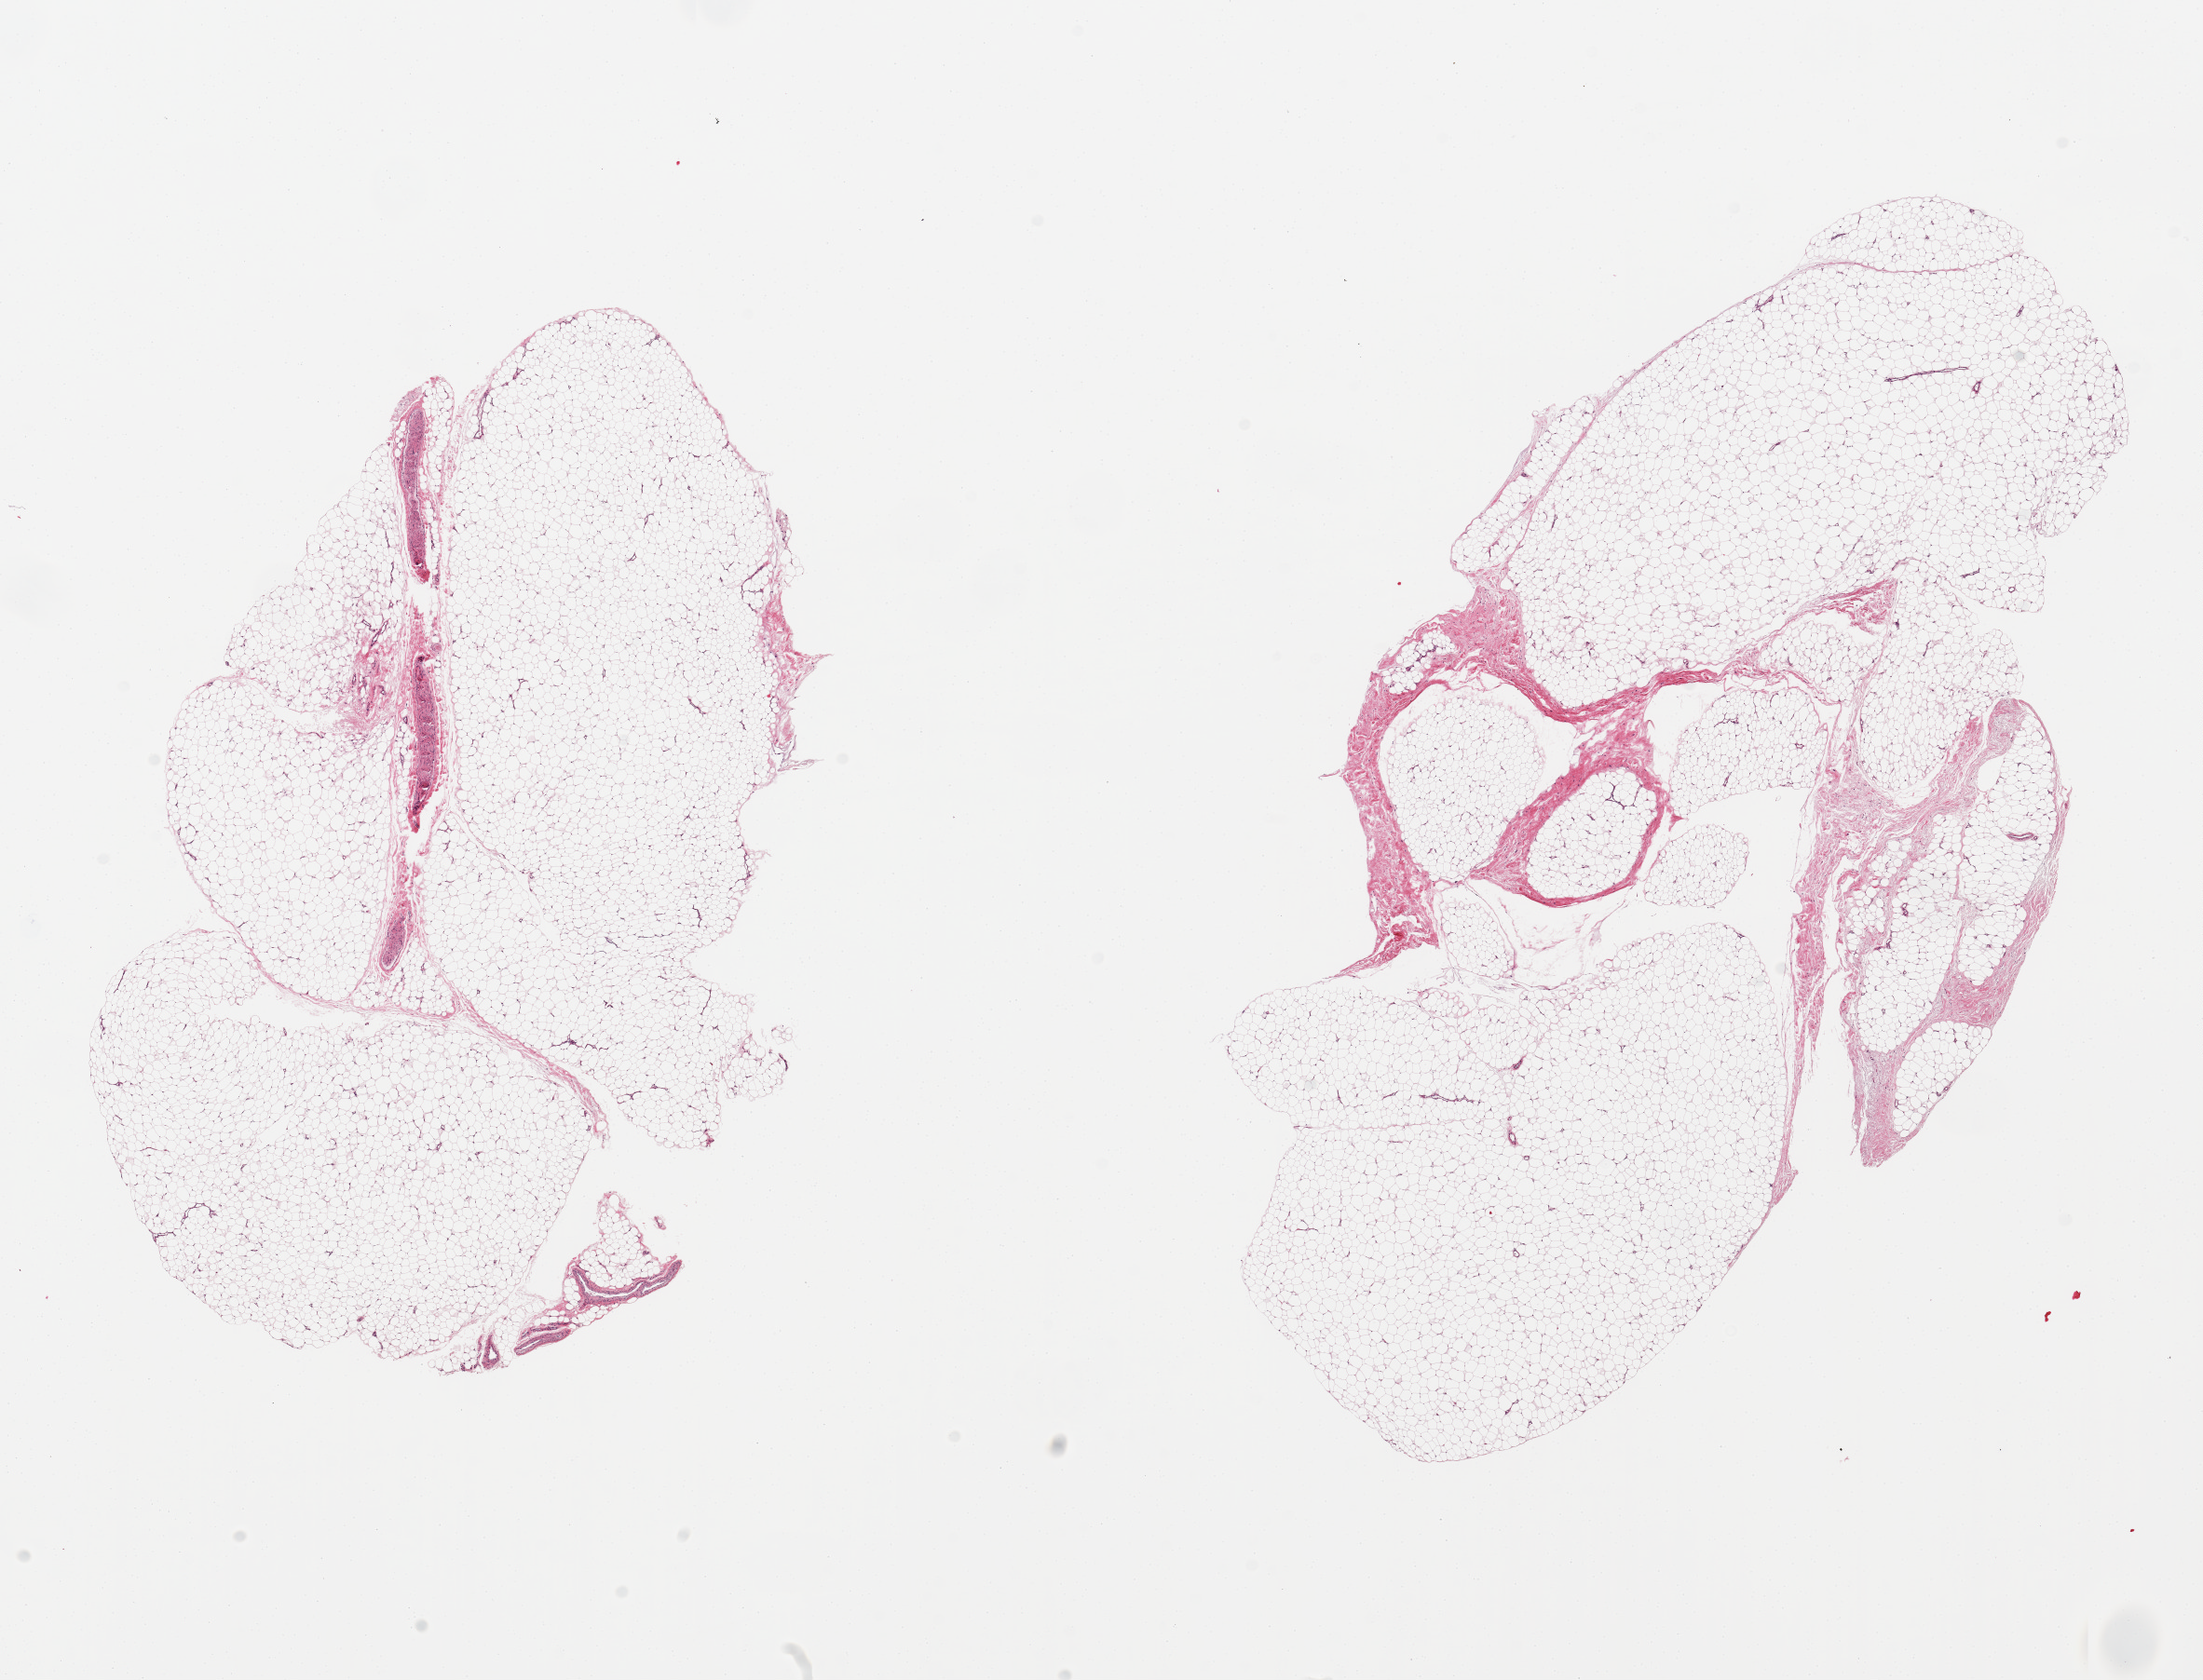
Haematoxylin and eosin whole-slide image, brightfield — low-resolution overview of the scanned area, about 18.7 x 14.3 mm. PAXgene-fixed paraffin-embedded (PFPE) section. Target tissue: adipose tissue. Donor tissue sample. Donor sex: male.
Review note (as recorded): 2 pieces; ~10%fascia/vascular elements and nerves.